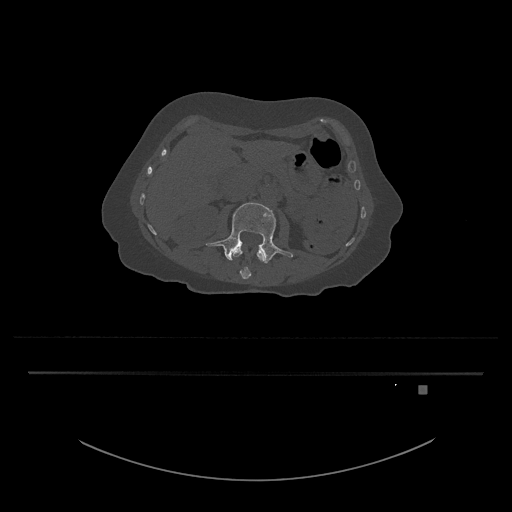
CT including the spine, one axial slice. Slice 446 of 797 in the series (ordered by position). 120 kVp. Bone window (W 1800 / L 400 HU). 512 × 512 image matrix, field of view 500 × 500 mm. Patient: female, 57 years. From the clinical record (not read from this slice): primary cancer: cervical.
Outlined on this slice (semi-automatic segmentation, software-assisted and operator-edited):
- L3 vertebra: bounding box <206,202,293,264> (left, top, right, bottom; pixels)